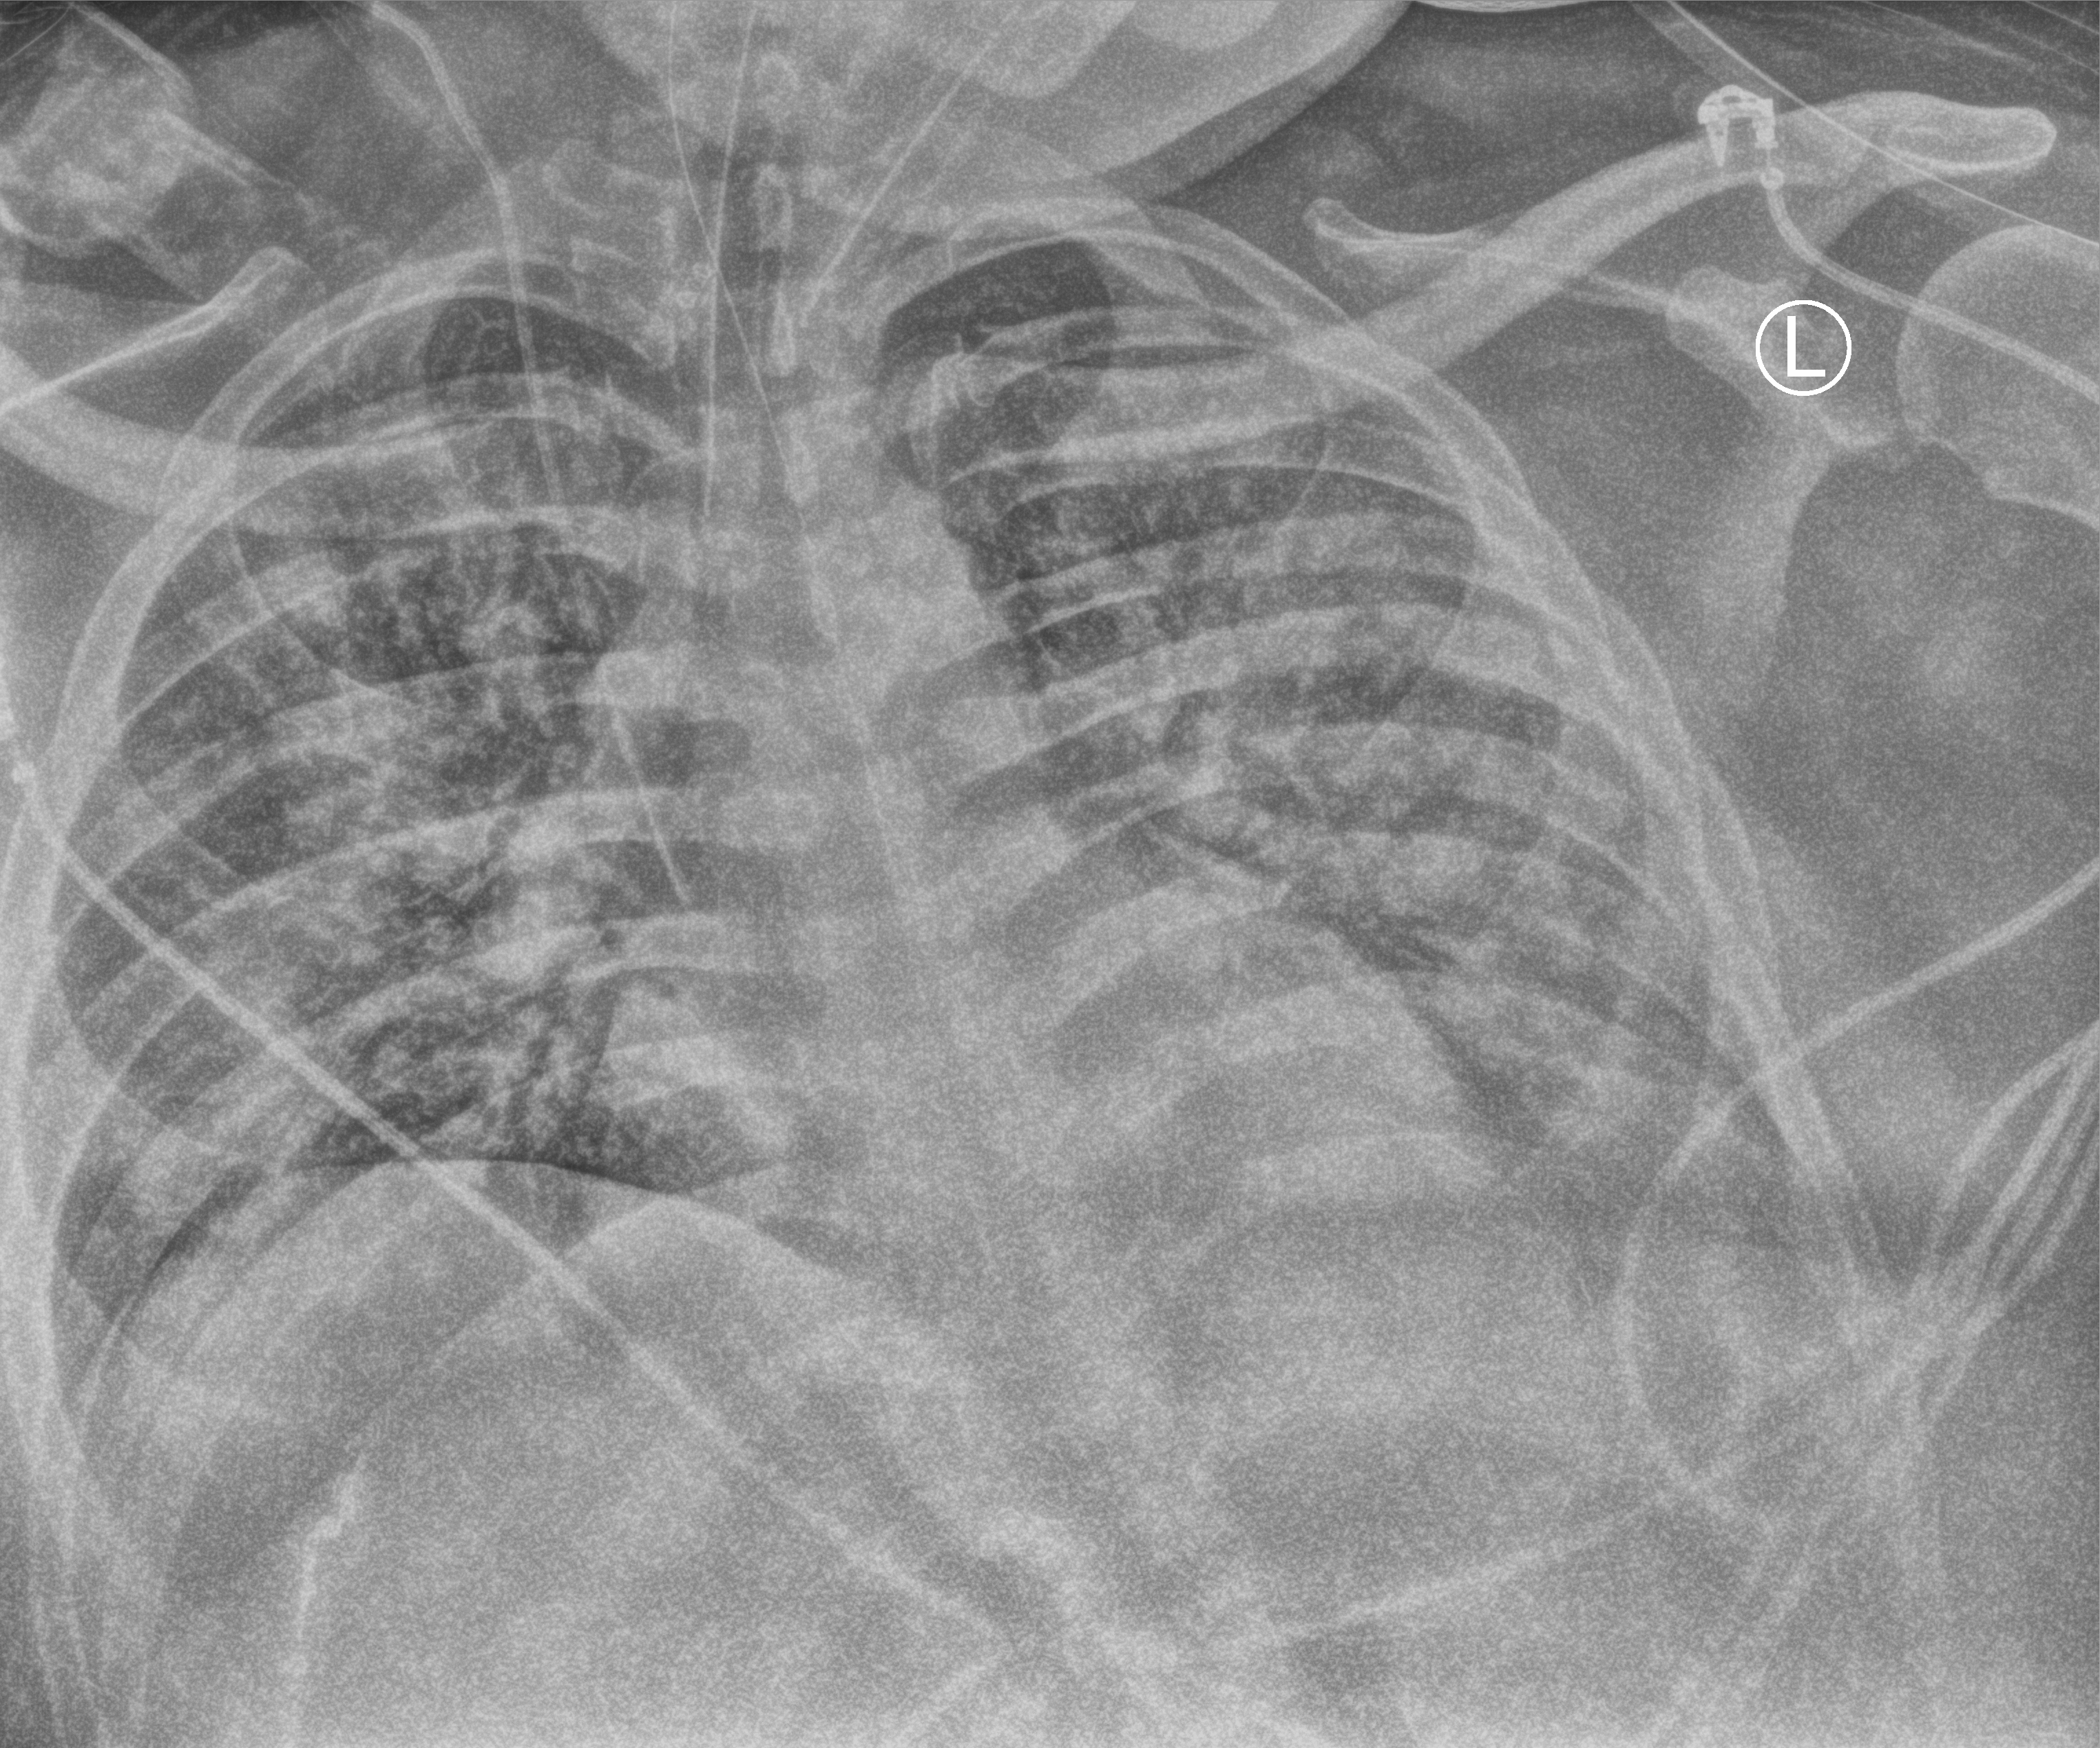
Chest X-ray (portable), anteroposterior (AP) projection. Patient hospitalised with COVID-19; male, aged 18–59 years.
From the hospital-stay record, not from the radiograph (when in the stay this image was taken is not recorded):
- length of hospital stay: 69 days